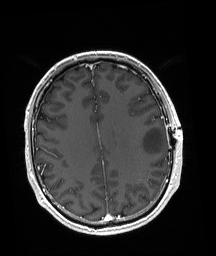
Brain MRI from a brain-tumour surgery series, one axial slice. Position 71 of 192 along the scan axis. T1-weighted post-contrast. 1 mm slice thickness. 216 × 256 image matrix, field of view 211 × 250 mm. Case-level facts recorded for this patient, not image findings: histopathology: Astrocytoma; WHO grade: 3; IDH mutation: yes; tumour location: Left Posterior Frontal.
Structures marked on this image (expert manual segmentation):
- tumour: bounding box <140,127,166,155> (left, top, right, bottom; pixels)